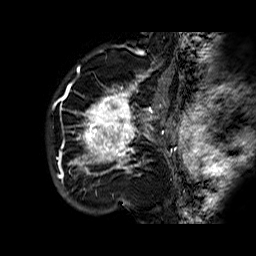
Breast MRI (dynamic contrast-enhanced), one sagittal slice. Slice 48 of 60 in the series (ordered by position). Dynamic contrast-enhanced series, time point 2 of 6 at this slice position (early post-contrast). 1.5 T. TE 6.3 ms, TR 32.4 ms. 4 mm slice thickness. 256 × 256 image matrix. Female patient. Case-level facts recorded for this patient, not image findings: setting: breast cancer imaged before/during neoadjuvant chemotherapy; receptor status: HR-positive, HER2-negative.
Structures marked on this image (semi-automatic segmentation, software-assisted and operator-edited):
- analysis volume of interest (the breast-tissue region the enhancement analysis was run in; not a lesion): bounding box <68,72,177,183> (left, top, right, bottom; pixels)
- tumour enhancement mask (voxels above the 100 % enhancement threshold inside the analysis volume of interest): <69,74,176,175>